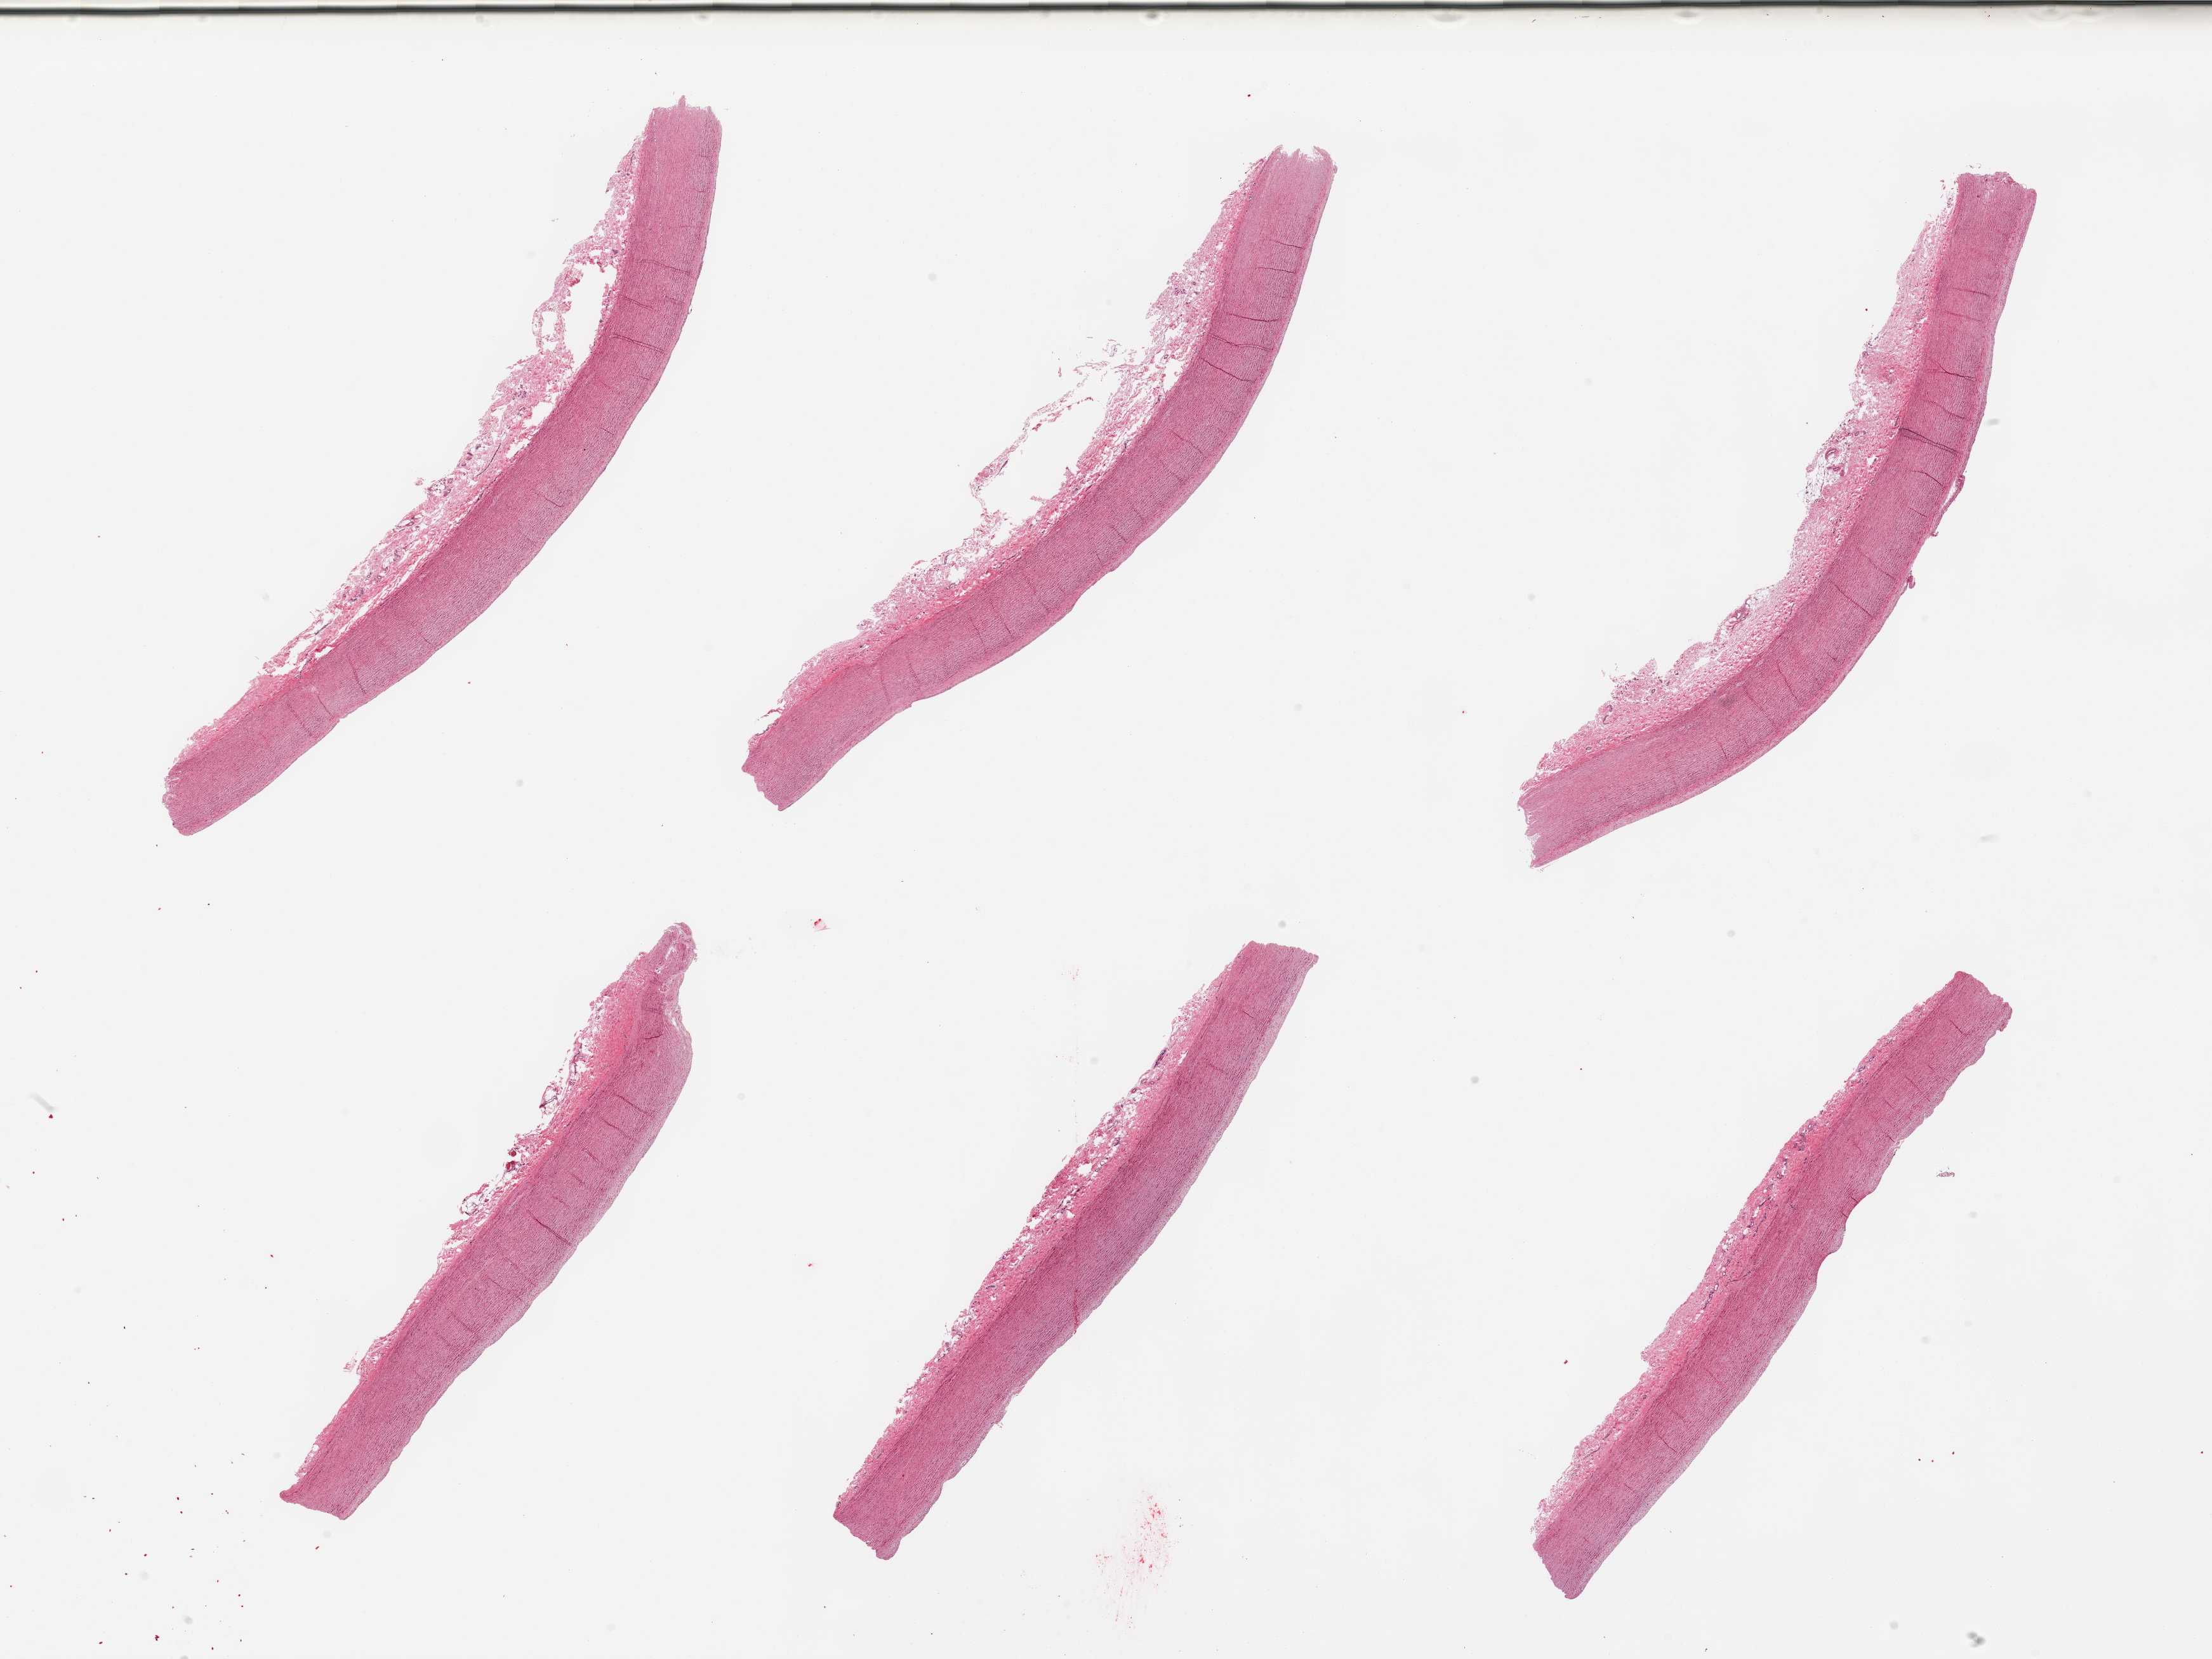
Digitized hematoxylin and eosin (H&E)-stained section — whole scanned area (about 27.6 x 20.7 mm) shown as a low-resolution overview; PAXgene-fixed paraffin-embedded (PFPE) section; target tissue: aorta; donor tissue sample. Donor: female.
Reviewer comment on this tissue sample: 6 pieces.